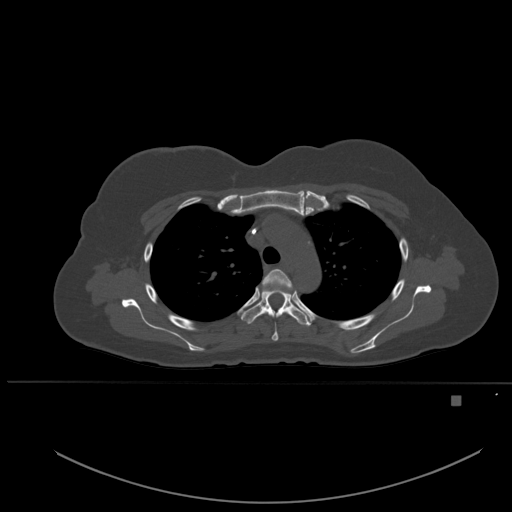
CT including the spine, one axial slice; position 384 of 651 along the scan axis; bone window (W 1800 / L 400 HU); 512 × 512 image matrix, field of view 443 × 443 mm. Female patient, age 49 years. From the clinical record (not read from this slice): primary cancer: breast.
Structures marked on this image (semi-automatic segmentation, software-assisted and operator-edited):
- T3 vertebra: bounding box [x1, y1, x2, y2] px = [262, 269, 292, 341]
- T4 vertebra: [240, 289, 311, 326]